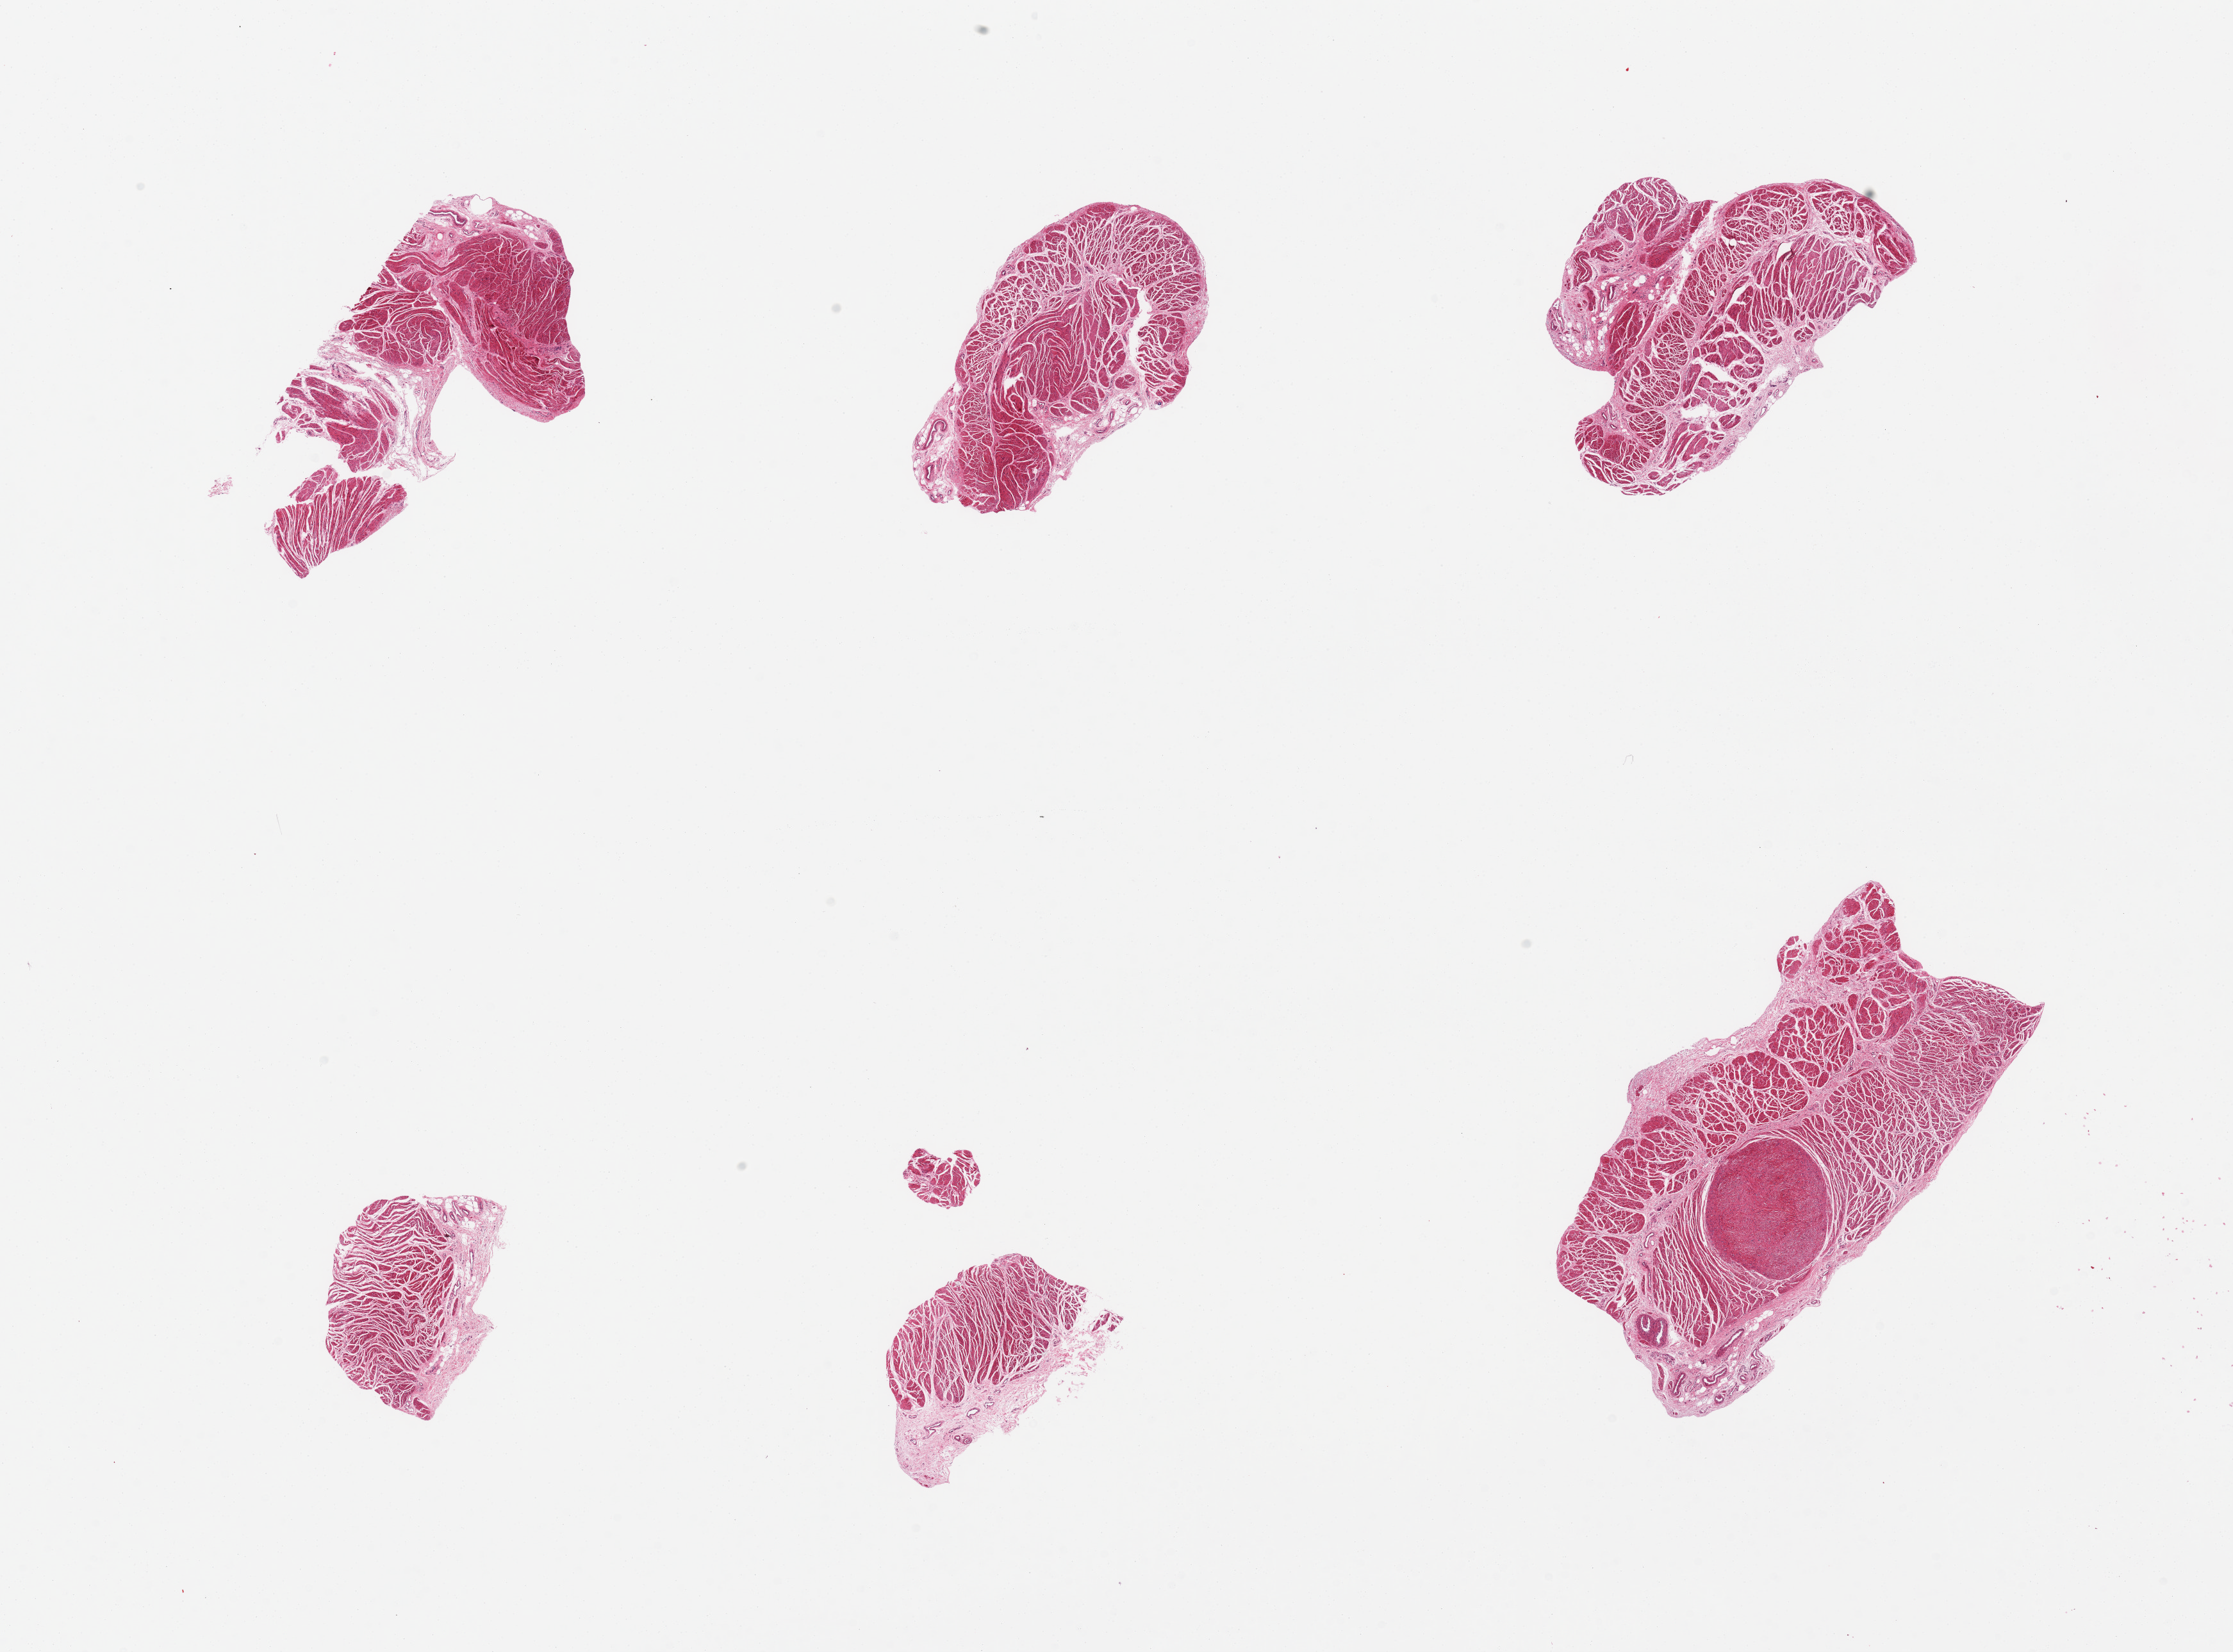
Whole-slide image, H&E stain — whole scanned area (about 27.6 x 20.4 mm) shown as a low-resolution overview; PAXgene-fixed paraffin-embedded (PFPE) section; target tissue: gastroesophageal junction; donor tissue sample. Female donor.
Reviewer comment on this tissue sample: 6 pieces; most are small, e.g. 3x2mm, largest 6x3mm.